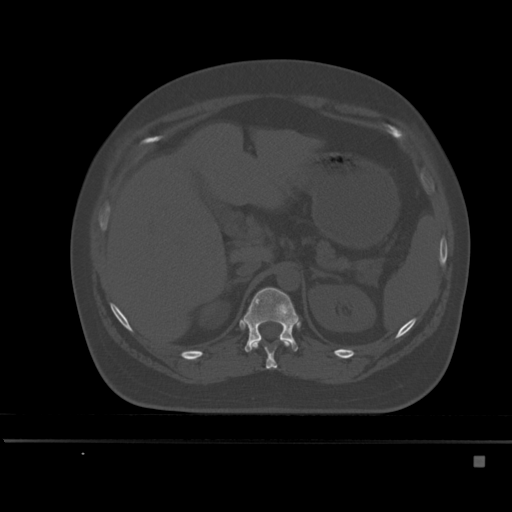
CT including the spine, one axial slice; slice 220 of 495 in the series (ordered by position); bone window (W 1800 / L 400 HU); 1.5 mm slice thickness; 512 × 512 image matrix, field of view 404 × 404 mm. Female patient, age 33 years. From the clinical record (not read from this slice): primary cancer: breast.
Annotated regions visible in this slice (semi-automatic segmentation, software-assisted and operator-edited):
- T11 vertebra: bounding box <250,341,291,369> (left, top, right, bottom; pixels)
- T12 vertebra: <242,287,298,352>